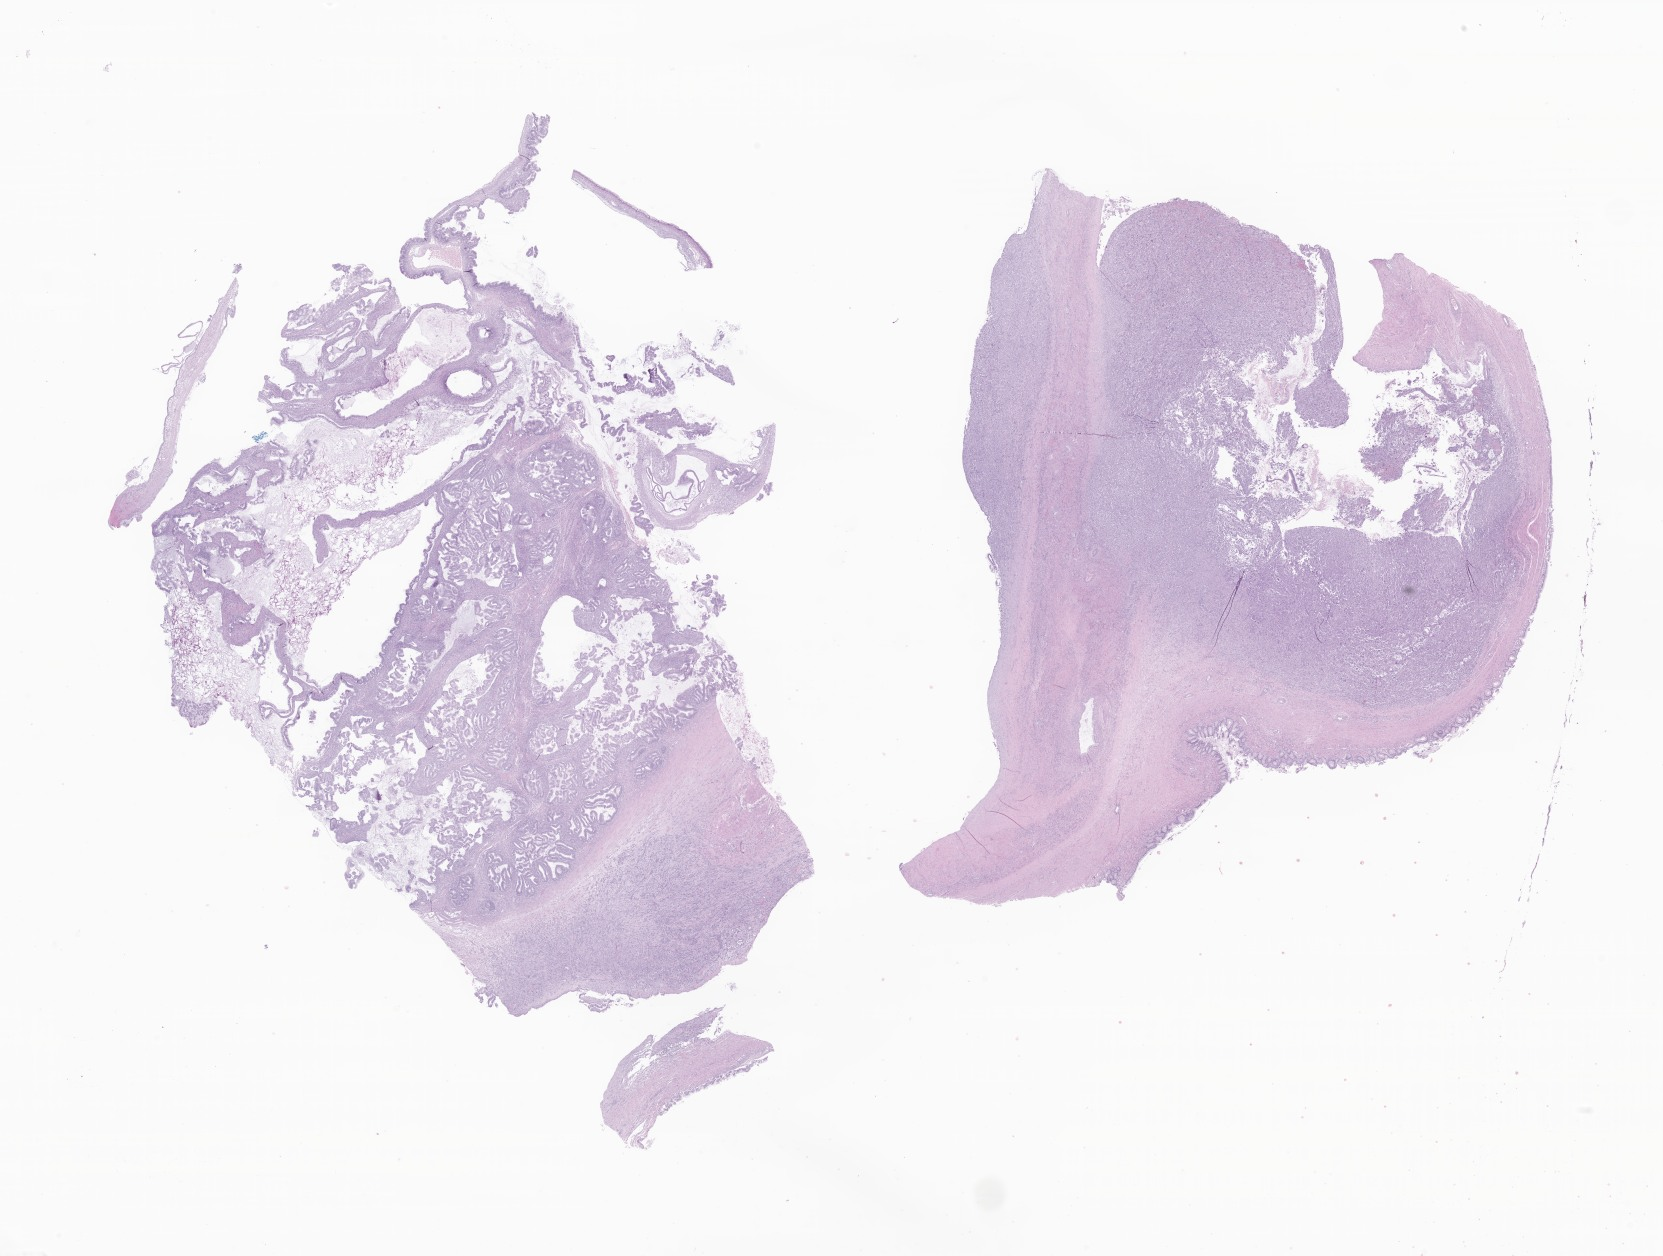
Digitized H&E-stained section of tumor tissue from the ovary, whole scanned area (about 28.0 x 21.2 mm) shown as a low-resolution overview; formalin-fixed, paraffin-embedded (FFPE) tissue. Patient female; age 182 months (15 years 2 months).
- diagnosis: Mucinous adenocarcinoma